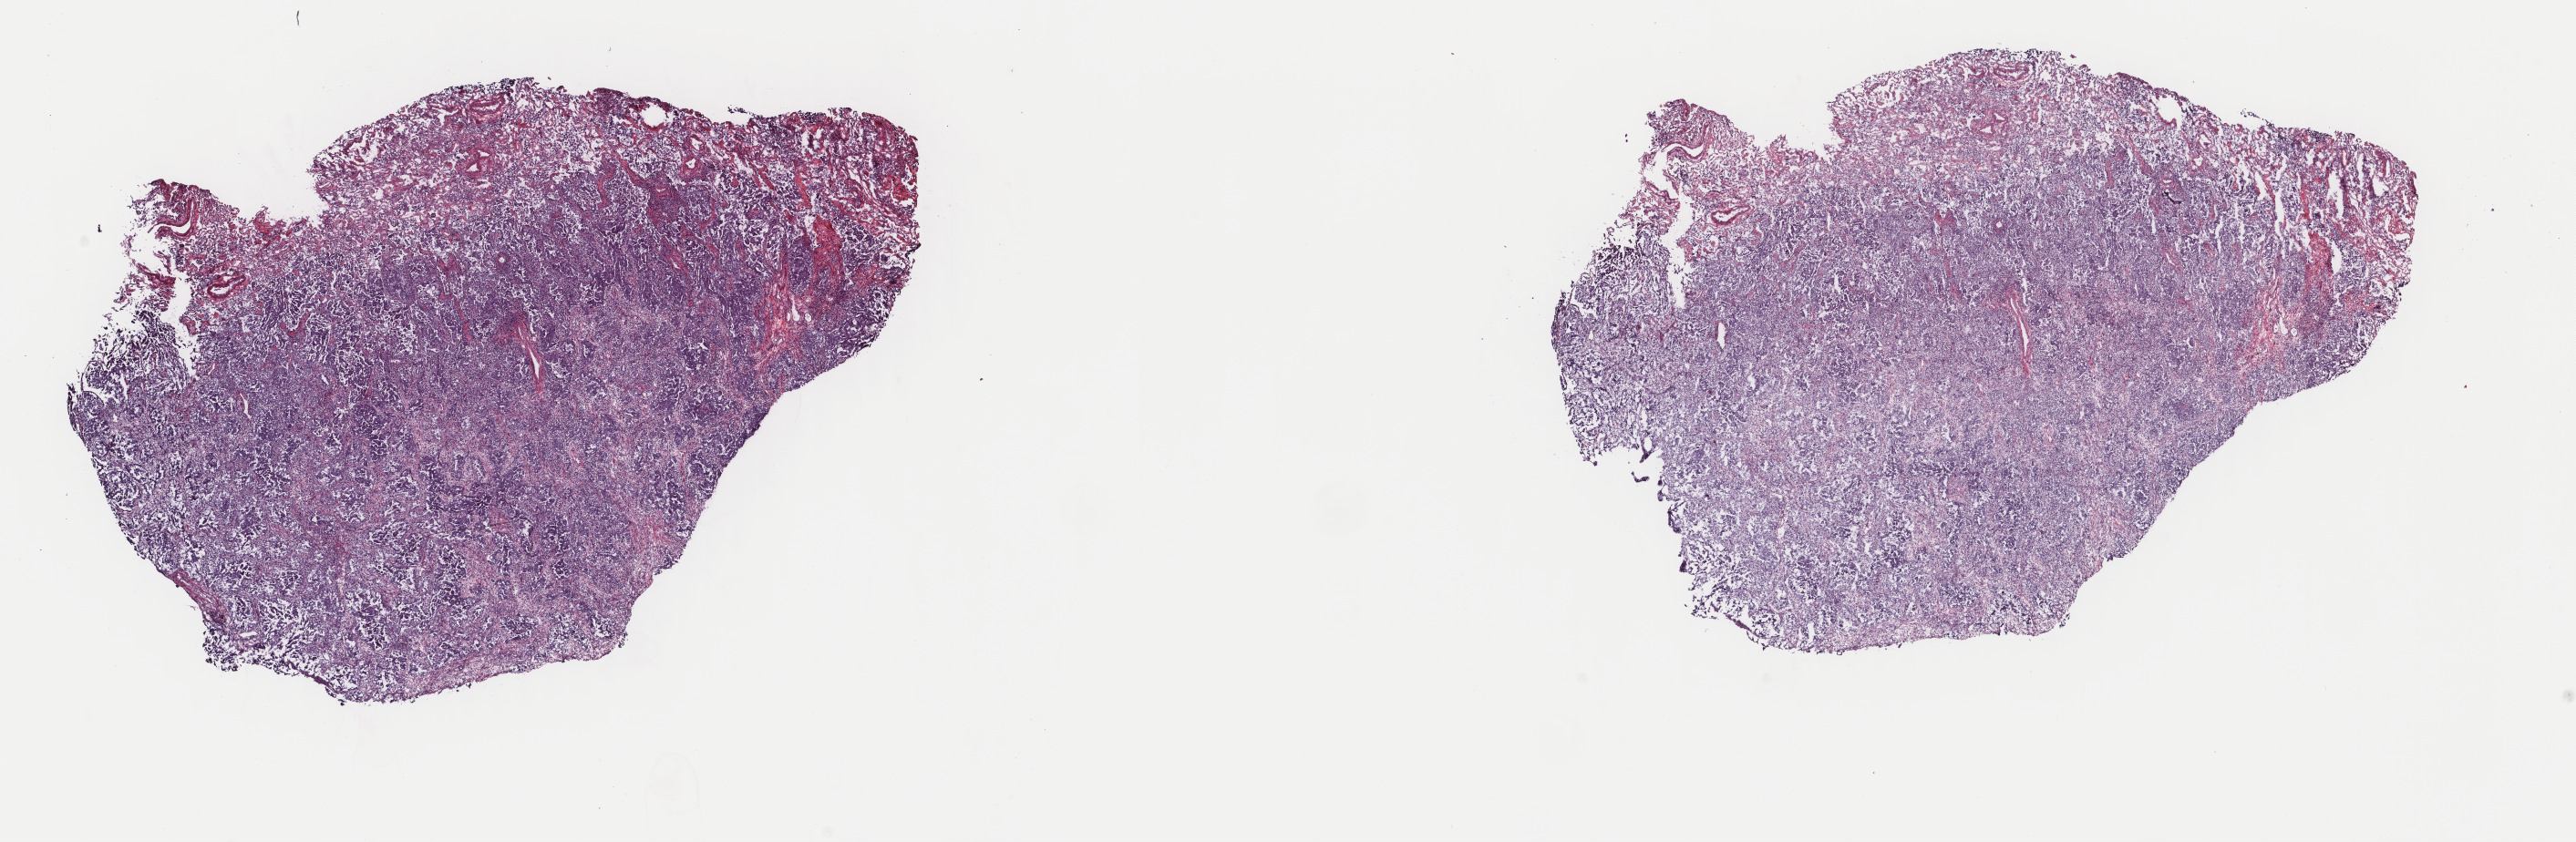
Digitized H&E tissue section (whole slide), low-resolution overview of the scanned area, about 22.4 x 7.3 mm (slide scanned at 40x), frozen section from the top of the tissue portion, sample: primary tumour, lung. Patient: male, age at initial diagnosis 70 years. Slide review estimates, as recorded: tumour cells 90%, tumour nuclei 70%, normal cells 10%, stromal cells 0%, necrosis 0%. Inflammatory infiltration, as recorded: lymphocyte infiltration 3%, monocyte infiltration 3%, neutrophil infiltration 0%.
• diagnosis: Adenocarcinoma, NOS (lower lobe, lung)
• AJCC pathologic stage: IIB (7th edition)
• TNM: T3 N0 M0
• laterality: right